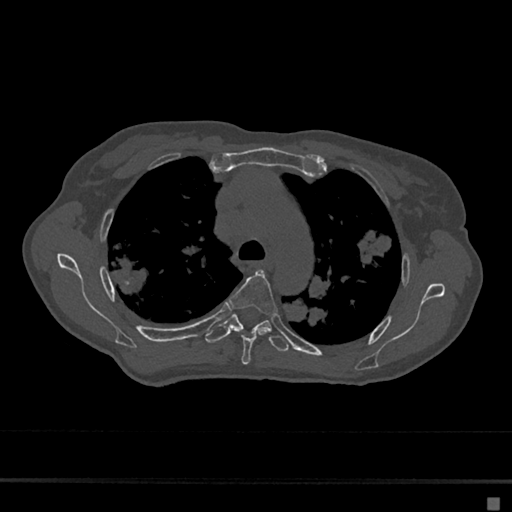
CT including the spine, one axial slice; position 485 of 797 along the scan axis; reconstruction kernel Br40s/3; bone window (W 1800 / L 400 HU); 0.5 mm slice thickness; 512 × 512 image matrix, field of view 360 × 360 mm. Patient: female, 68 years. Case-level facts recorded for this patient, not image findings: primary cancer: renal.
Structures marked on this image (semi-automatically segmented with operator editing):
- T4 vertebra: bounding box [x1, y1, x2, y2] px = [228, 269, 278, 365]
- T5 vertebra: [205, 311, 288, 352]